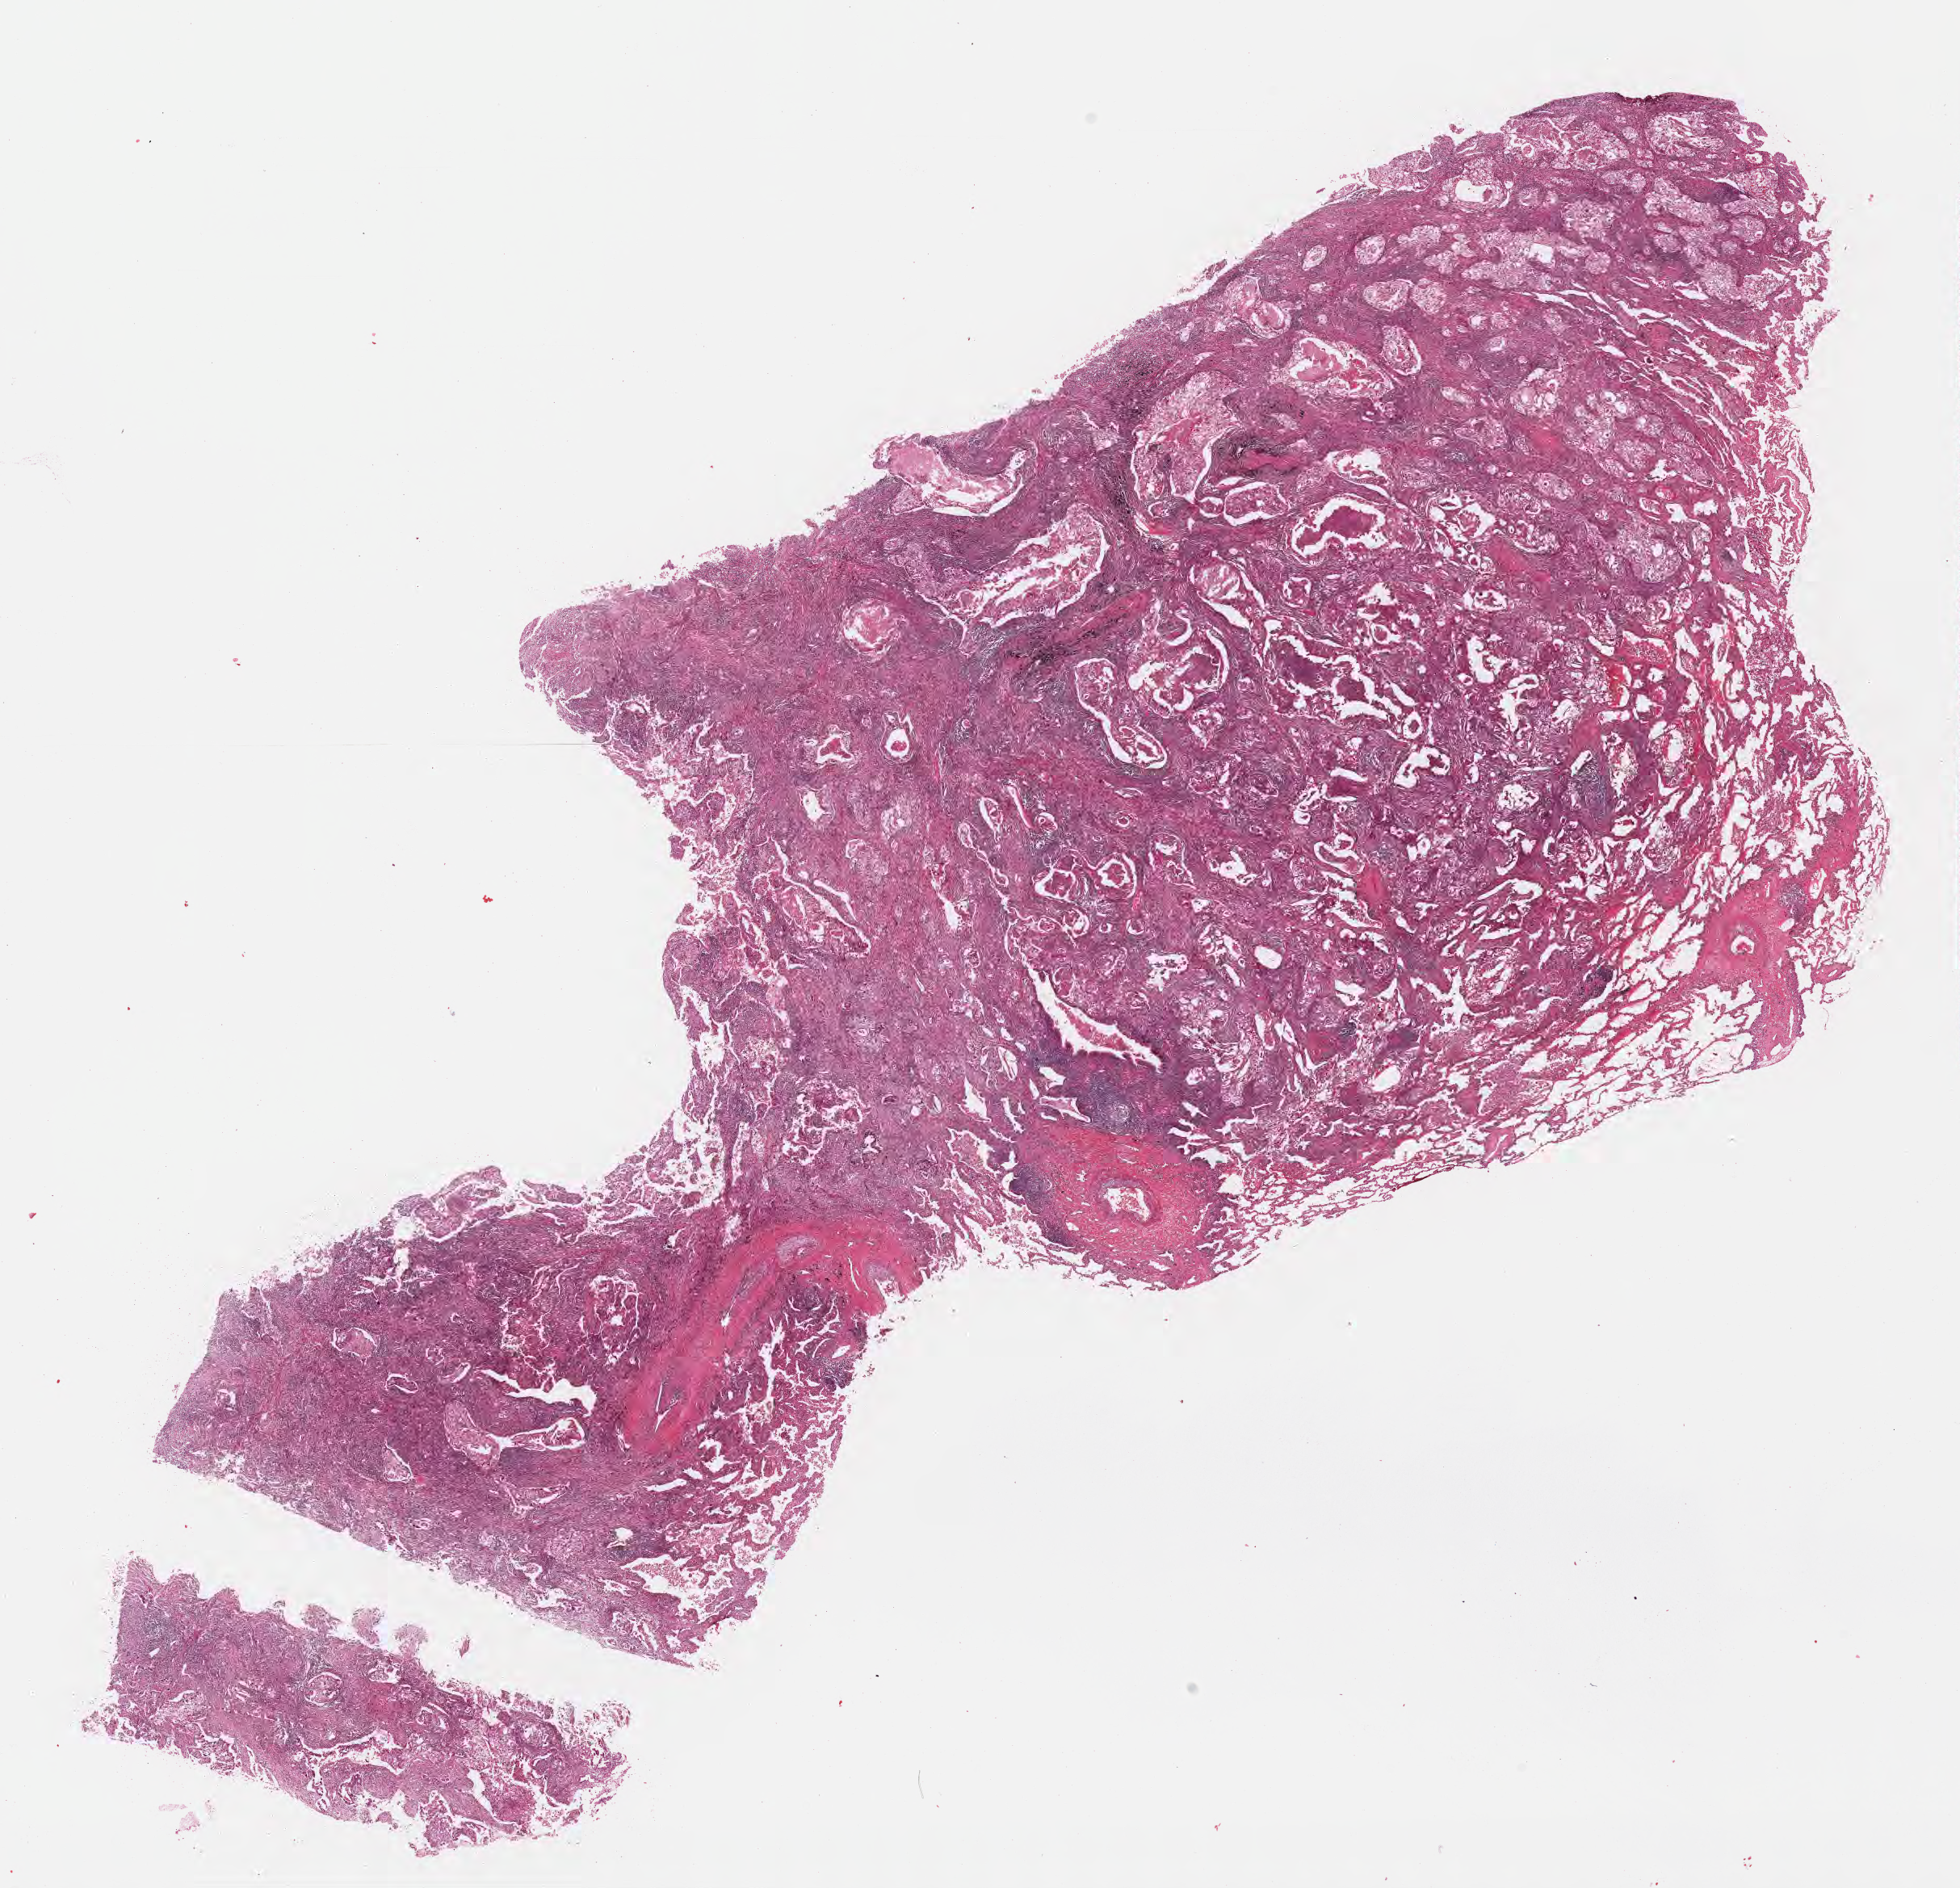
Whole-slide image, hematoxylin and eosin (H&E) stain, a low-resolution overview of the entire scanned area, about 19.6 x 18.9 mm; formalin-fixed paraffin-embedded section; specimen: primary tumor; site: upper lobe of right lung. Patient male; aged 73. Pathologist review of this section (percent, as recorded): tumor cells 90%, tumor nuclei 60%, stromal cells 0%, necrosis 5%, normal cells 5%. Infiltration values recorded for this section: lymphocyte infiltration 0%, monocyte infiltration 0%, neutrophil infiltration 0%.
Diagnosis: Adenocarcinoma, NOS. AJCC pathologic stage: Stage IB.